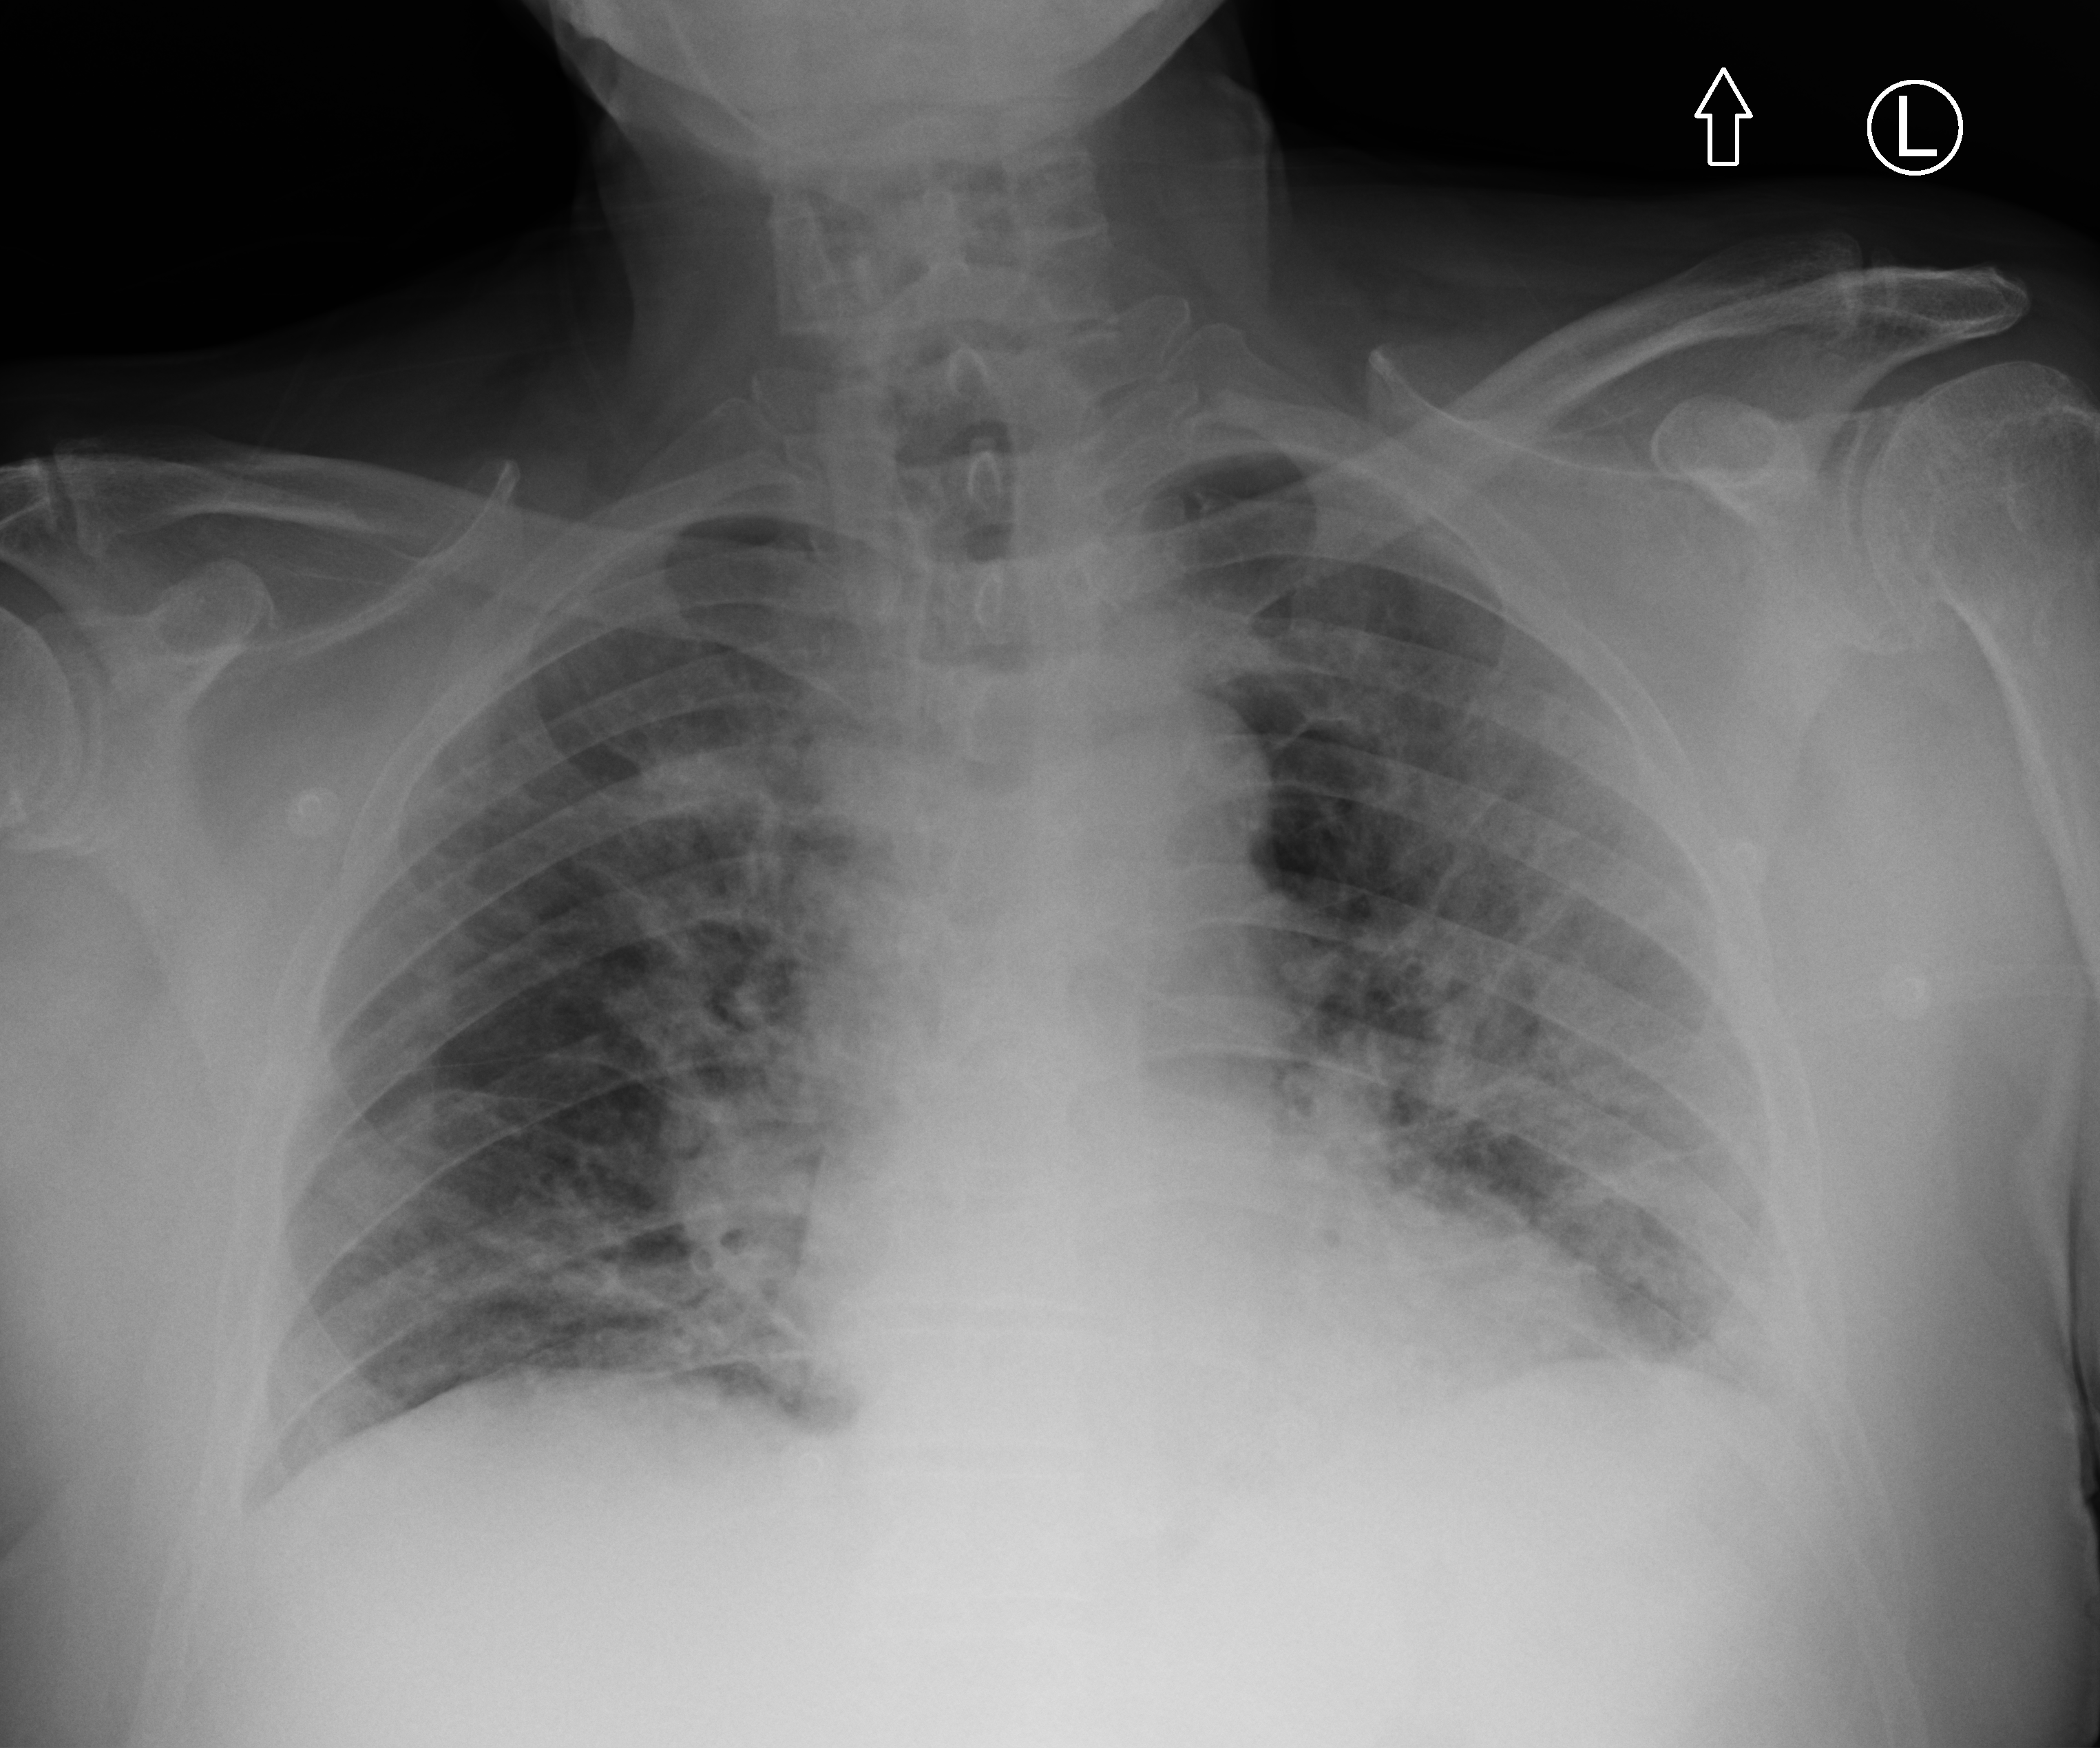
Bedside chest radiograph (computed radiography), anteroposterior (AP) projection. Male patient hospitalised with COVID-19, age 60–74 years.
Admission-level facts for this patient (not findings on this image; timing relative to this image not recorded): admitted to intensive care during this hospital stay: no; other chronic lung disease (admission record): no; length of hospital stay: 20 days.